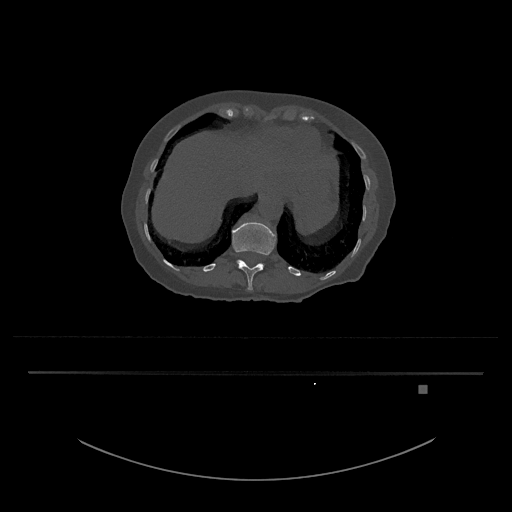
CT including the spine, one axial slice; reconstruction kernel Br40s/3; 120 kVp; bone window (W 1800 / L 400 HU); 0.5 mm slice thickness; 512 × 512 image matrix, field of view 500 × 500 mm. Patient: female, 57 years. From the clinical record (not read from this slice): primary cancer: cervical.
Annotated regions visible in this slice (semi-automatic segmentation, software-assisted and operator-edited):
- T12 vertebra: bounding box [x1, y1, x2, y2] px = [232, 222, 276, 291]